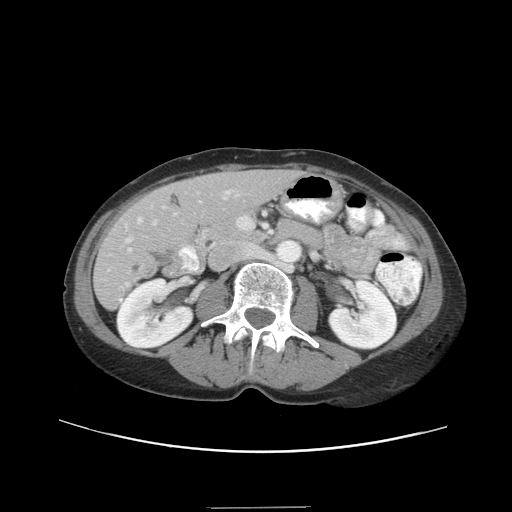
Contrast-enhanced abdominal CT, one axial slice. Slice 14 of 38 in the series (ordered by position). Intravenous contrast given. Soft-tissue window (W 400 / L 40 HU). 5 mm slice thickness. 512 × 512 image matrix, field of view 388 × 388 mm. Female patient, age 64 years. From the clinical record (not read from this slice): diagnosis: colorectal cancer liver metastases, imaged before liver resection; multiple liver metastases: no; largest metastasis: 3.8 cm.
Annotated regions visible in this slice (outlined manually by an expert reader):
- hepatic veins: bounding box [x1, y1, x2, y2] px = [126, 194, 239, 243]
- liver: [95, 172, 298, 307]
- planned liver remnant (the part of the liver to remain after resection): [146, 171, 299, 232]
- portal vein (with intrahepatic branches): [125, 190, 233, 252]